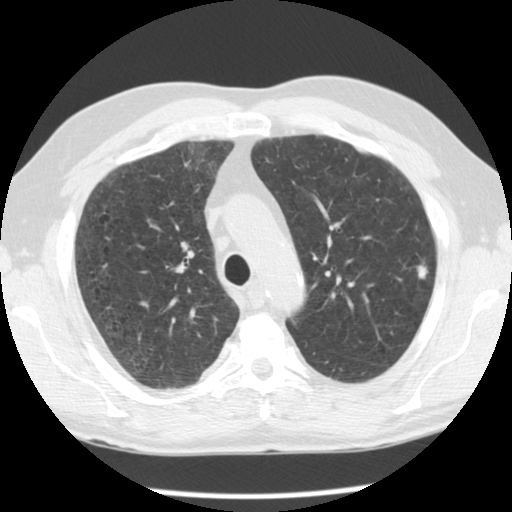
Low-dose screening chest CT, one axial slice; slice 84 of 113 in the series (ordered by position); reconstruction kernel STANDARD; 120 kVp; lung window (W 1500 / L -600 HU); 512 × 512 image matrix, field of view 330 × 330 mm.
Outlined on this slice (expert manual segmentation):
- lesion 3 (tumor, upper lobe of left lung): bounding box [x1, y1, x2, y2] px = [417, 264, 428, 279]